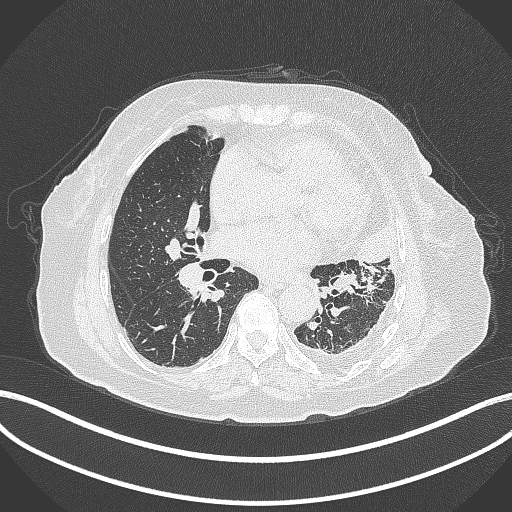
Chest CT, one axial slice; slice 173 of 399 in the series (ordered by position); 120 kVp; lung window (W 1500 / L -600 HU); 1 mm slice thickness; 512 × 512 image matrix, field of view 400 × 400 mm. Patient: female, 75 years. From the clinical record (not read from this slice): clinical TNM (as recorded): T3 N3 M1.
Annotated regions visible in this slice (bounding box drawn by a radiologist):
- lung tumour (recorded histology: adenocarcinoma): bounding box (x1, y1, x2, y2) in pixels: (355, 216, 402, 269)